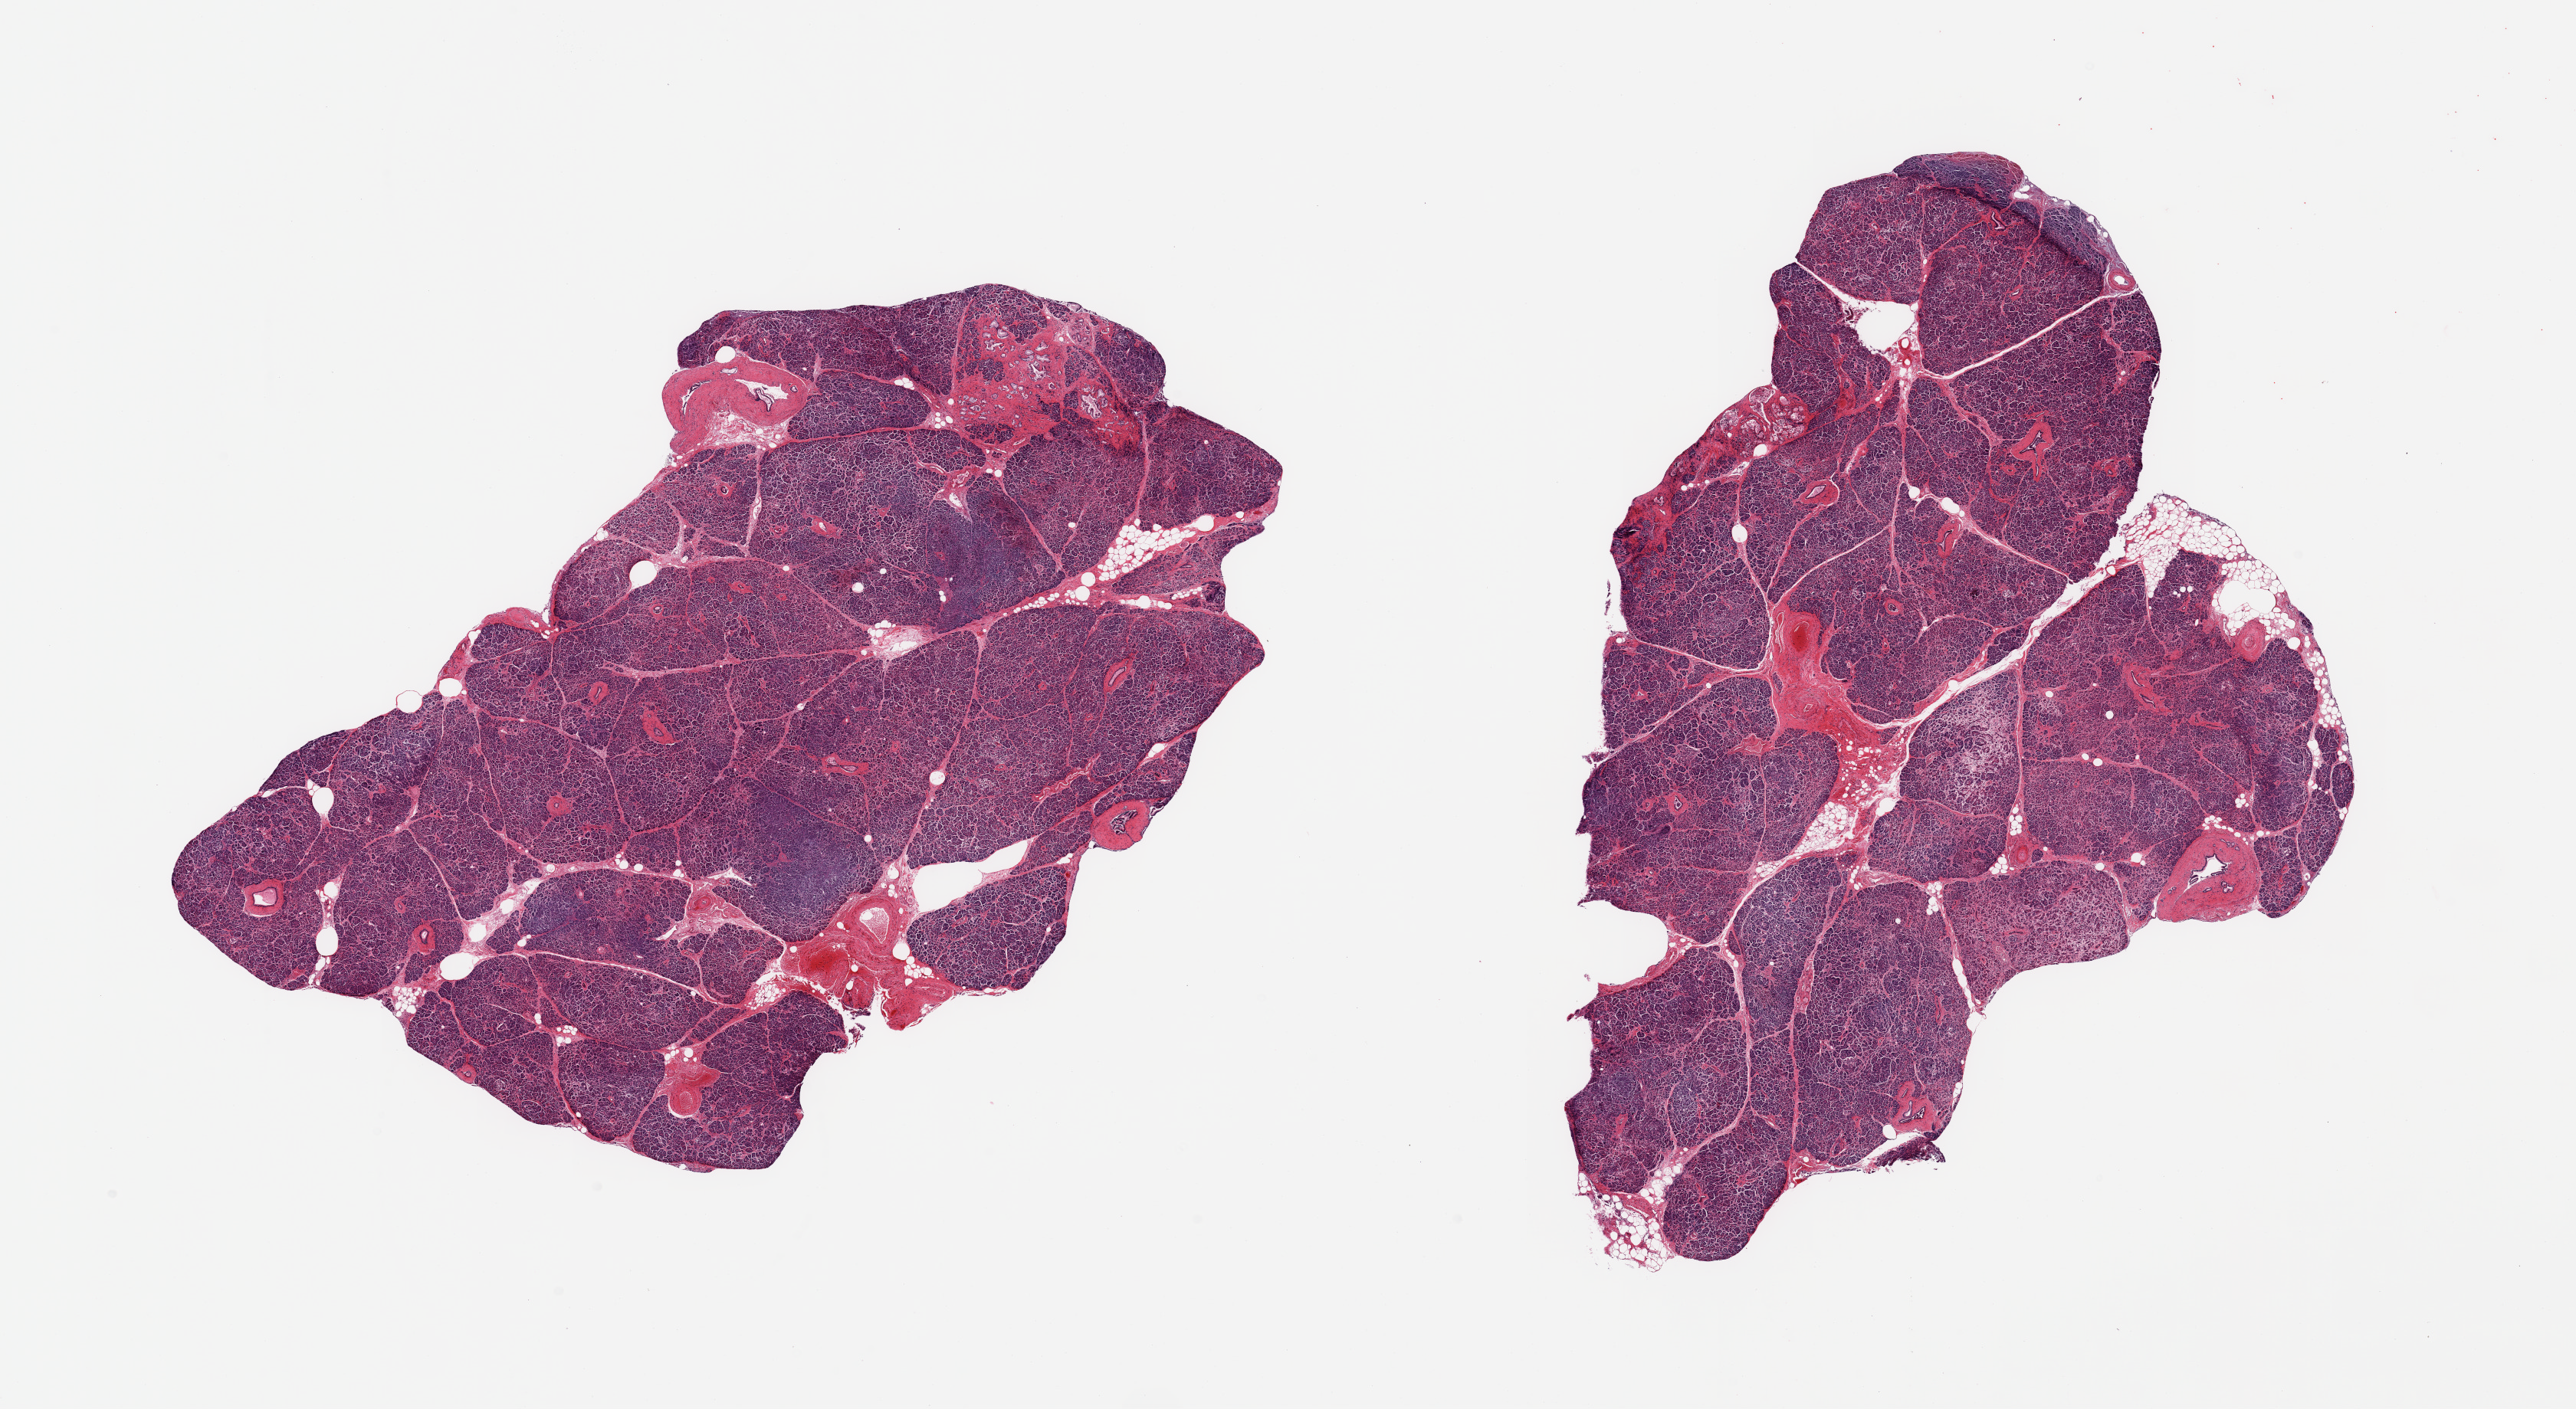
Digitized hematoxylin and eosin (H&E)-stained section, shown as a low-resolution overview of the whole scanned area (about 26.6 x 14.5 mm), PAXgene-fixed, paraffin-embedded tissue, target tissue: pancreas, donor tissue sample.
Reviewer comment on this tissue sample: 2 pieces, moderately advanced saponification, Islets not well-visualized.